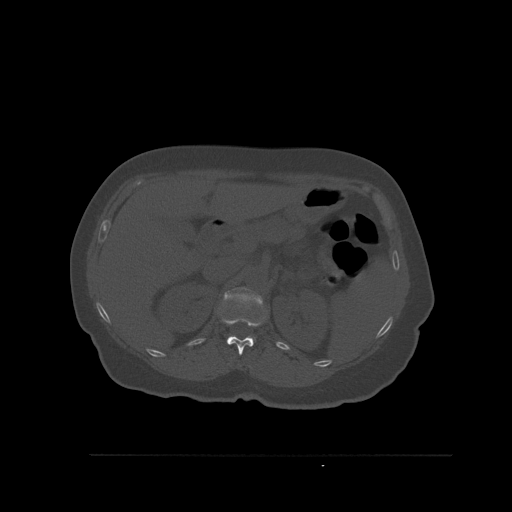
CT including the spine, one axial slice. Position 280 of 527 along the scan axis. Bone window (W 1800 / L 400 HU). 1.5 mm slice thickness. 512 × 512 image matrix, field of view 470 × 470 mm. Patient: female, 73 years. Case-level facts recorded for this patient, not image findings: primary cancer: breast.
Outlined on this slice (semi-automatic segmentation, software-assisted and operator-edited):
- L1 vertebra: box from (x=223, y=287) to (x=263, y=344) px
- T12 vertebra: (x=221, y=318)–(x=262, y=355)